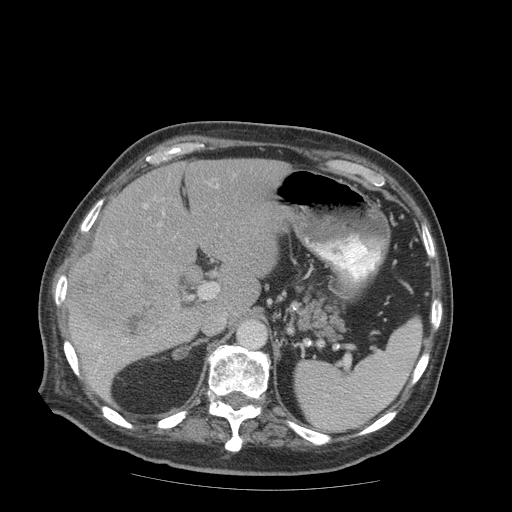
Contrast-enhanced abdominal CT (liver protocol), one axial slice. Reconstruction kernel STANDARD. 140 kVp. Soft-tissue window (W 400 / L 40 HU). 2.5 mm slice thickness. 512 × 512 image matrix, field of view 420 × 420 mm. From the clinical record (not read from this slice): diagnosis: hepatocellular carcinoma (patient treated with transarterial chemoembolisation; whether this scan precedes or follows treatment is not stated here); TNM stage (as recorded): Stage-IIIB.
Annotated regions visible in this slice (semi-automatic segmentation, software-assisted and operator-edited):
- liver parenchyma outside the tumour (the mass and vessels are separate outlines, so this box may not span the whole liver): box from (x=66, y=158) to (x=291, y=398) px
- mass: (x=68, y=246)–(x=179, y=345)
- liver vessels: (x=95, y=185)–(x=217, y=372)